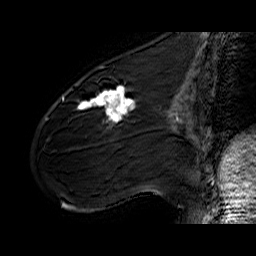
Breast MRI (dynamic contrast-enhanced), one sagittal slice. Dynamic contrast-enhanced series, time point 2 of 6 at this slice position (early post-contrast). 1.5 T. TE 6.4 ms, TR 32.9 ms. 4 mm slice thickness. 256 × 256 image matrix, field of view 200 × 200 mm. Female patient. Case-level facts recorded for this patient, not image findings: setting: breast cancer imaged before/during neoadjuvant chemotherapy; receptor status: HER2-positive.
Structures marked on this image (semi-automatically segmented with operator editing):
- analysis volume of interest (the breast-tissue region the enhancement analysis was run in; not a lesion): bounding box <61,77,141,142> (left, top, right, bottom; pixels)
- tumour enhancement mask (voxels above the 100 % enhancement threshold inside the analysis volume of interest): <62,86,137,126>